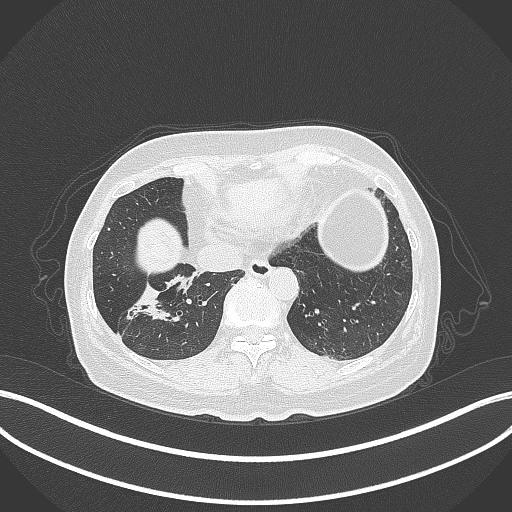
Chest CT, one axial slice; slice 105 of 429 in the series (ordered by position); reconstruction kernel B70f; 120 kVp; lung window (W 1500 / L -600 HU); 512 × 512 image matrix, field of view 400 × 400 mm. Female patient, age 67 years. From the clinical record (not read from this slice): clinical TNM (as recorded): T1c N1 M0.
Outlined on this slice (bounding box drawn by a radiologist):
- lung tumour (recorded histology: adenocarcinoma): box from (x=116, y=272) to (x=191, y=331) px